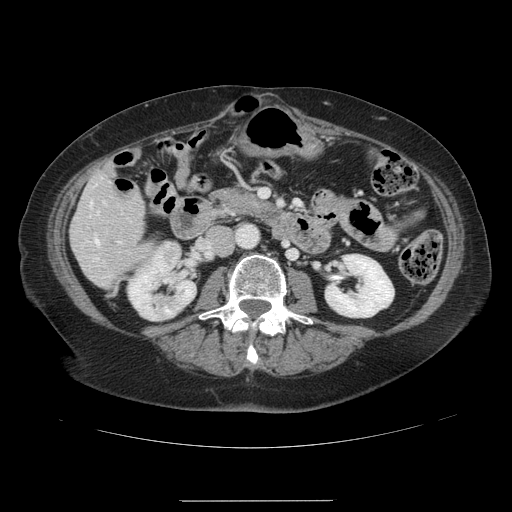
Contrast-enhanced abdominal CT, one axial slice. Slice 38 of 141 in the series (ordered by position). Intravenous contrast given. Soft-tissue window (W 400 / L 40 HU). 2.5 mm slice thickness. 512 × 512 image matrix. Female patient, age 74 years. Case-level facts recorded for this patient, not image findings: diagnosis: colorectal cancer liver metastases, imaged before liver resection; multiple liver metastases: yes; largest metastasis: 7 cm; disease in both lobes: yes.
Outlined on this slice (expert manual segmentation):
- hepatic veins: bounding box [x1, y1, x2, y2] px = [90, 202, 98, 244]
- liver: [72, 173, 151, 288]
- planned liver remnant (the part of the liver to remain after resection): [82, 173, 151, 286]
- portal vein (with intrahepatic branches): [104, 202, 120, 242]